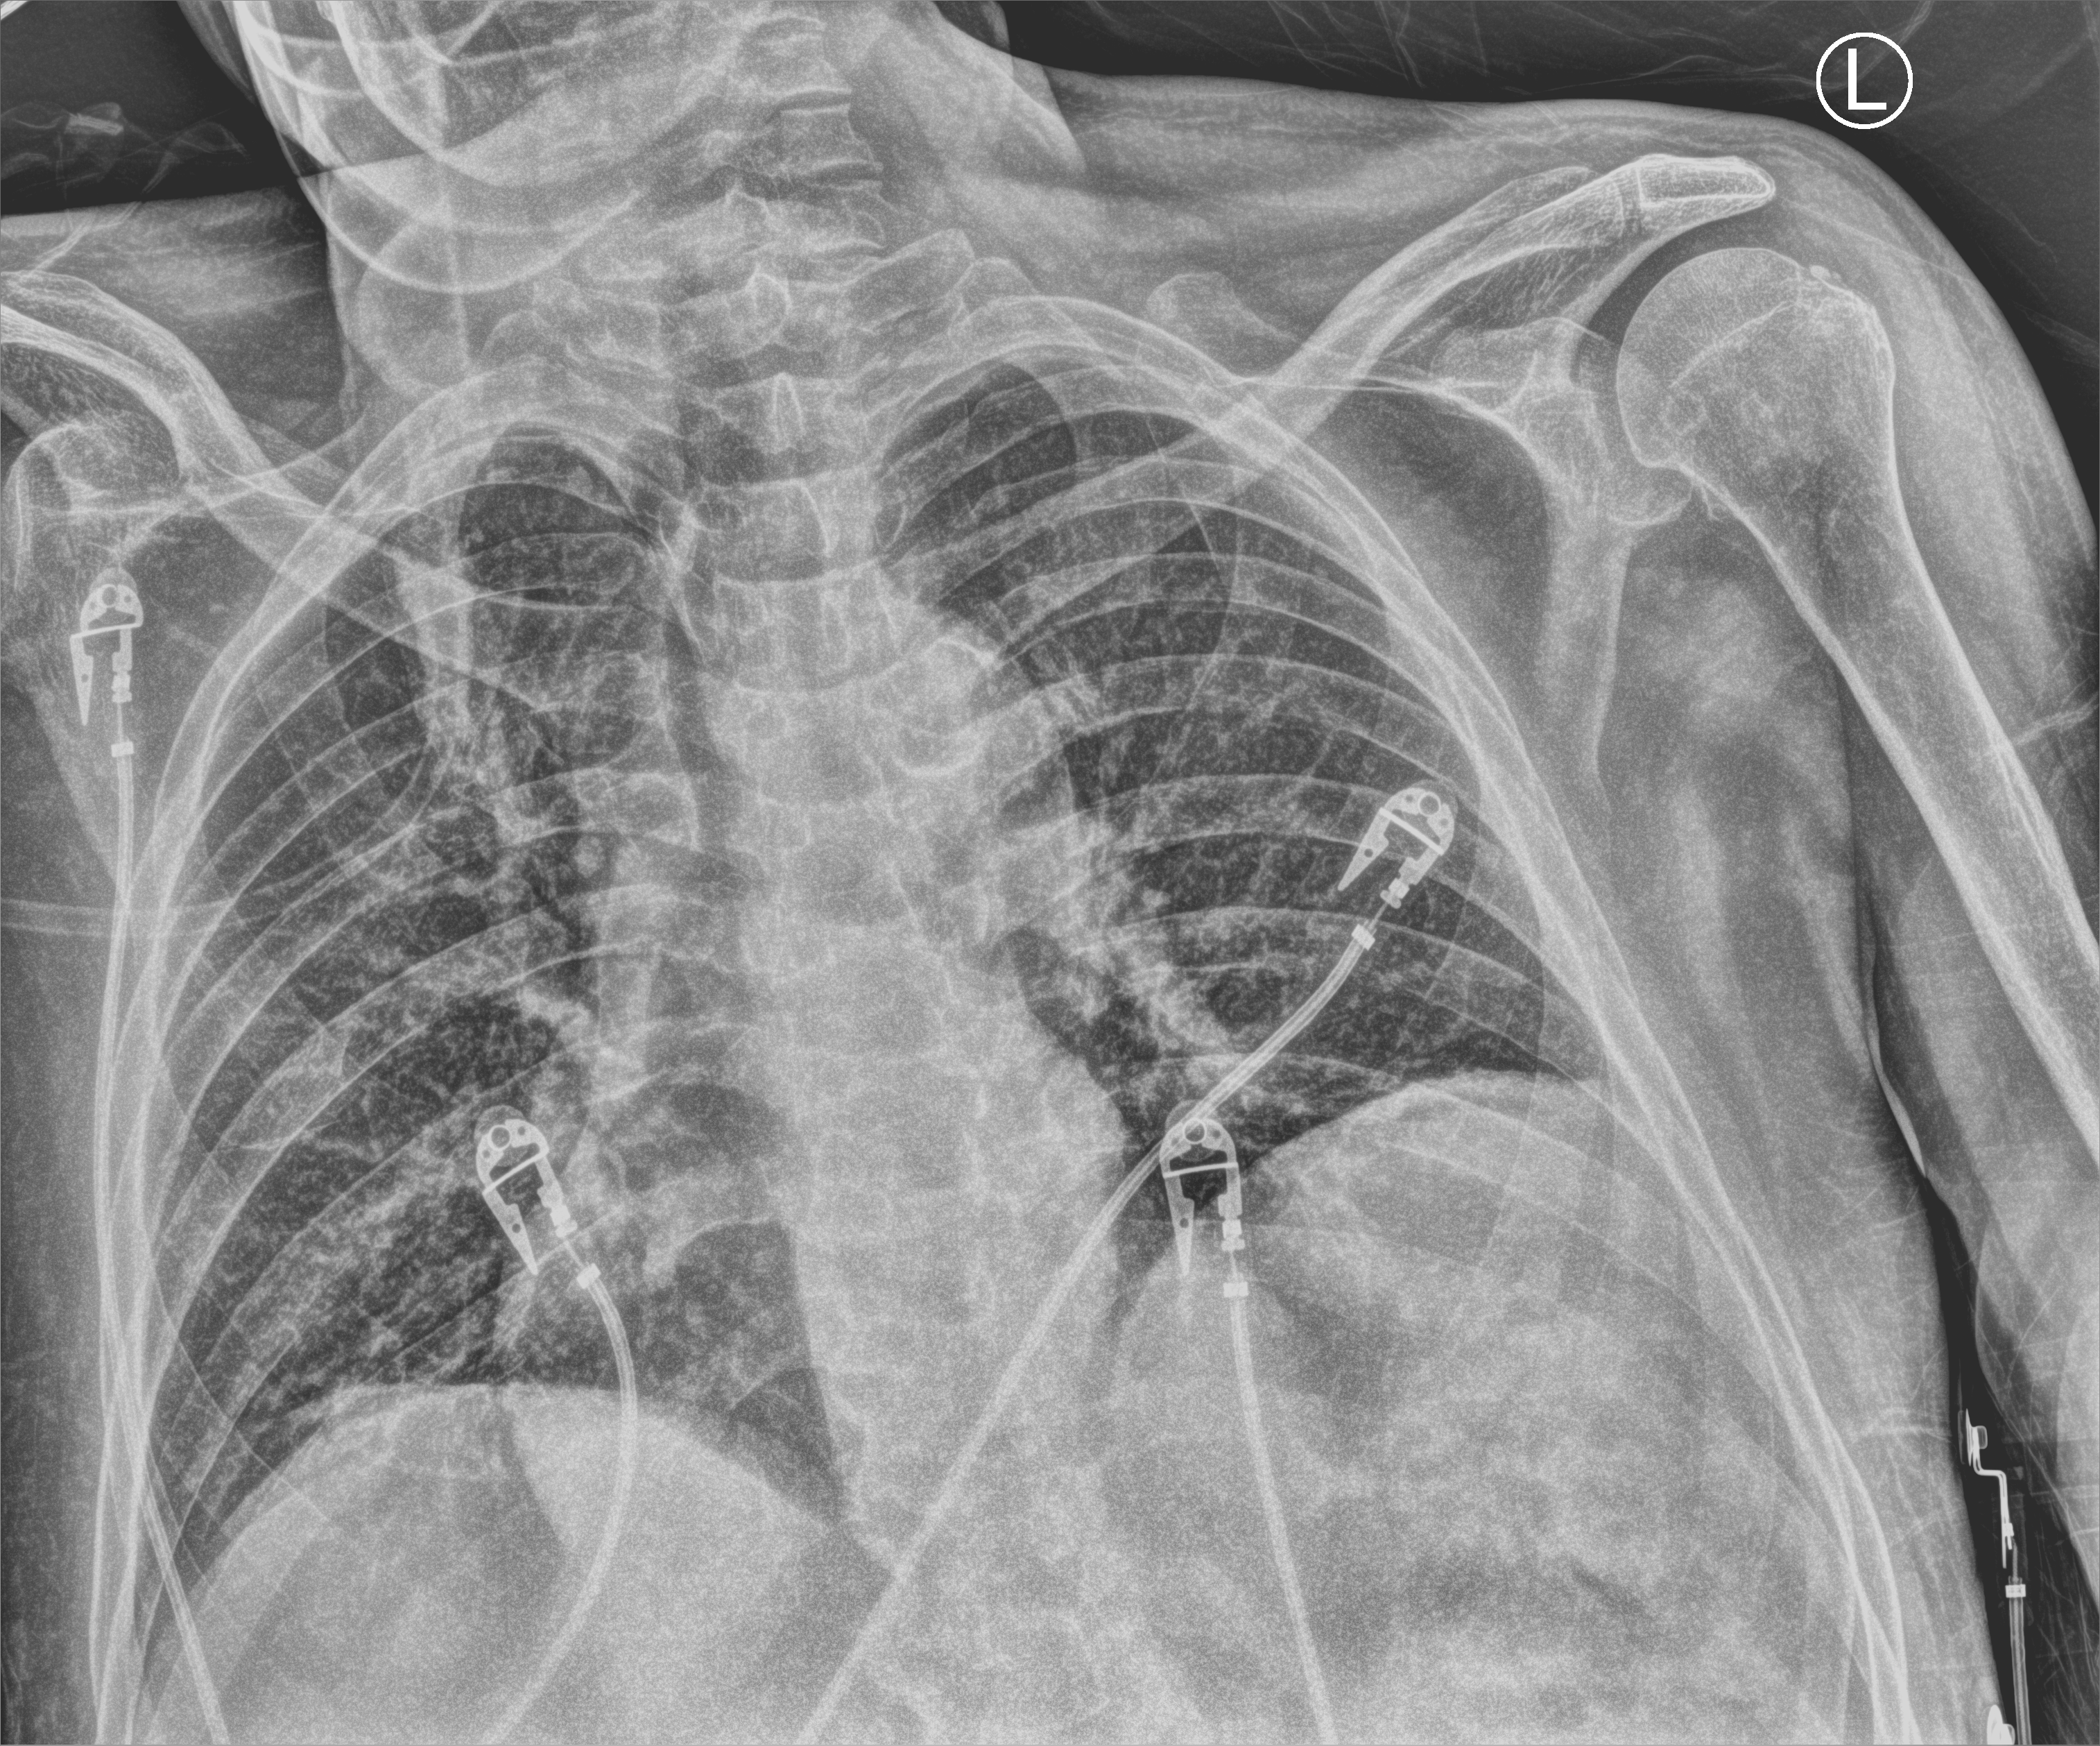
Chest X-ray (portable); anteroposterior (AP) projection. Male patient hospitalised with COVID-19, age 75–90 years.
Admission-level facts for this patient (not findings on this image; timing relative to this image not recorded): other chronic lung disease (admission record): no; chronic kidney disease (admission record): yes.